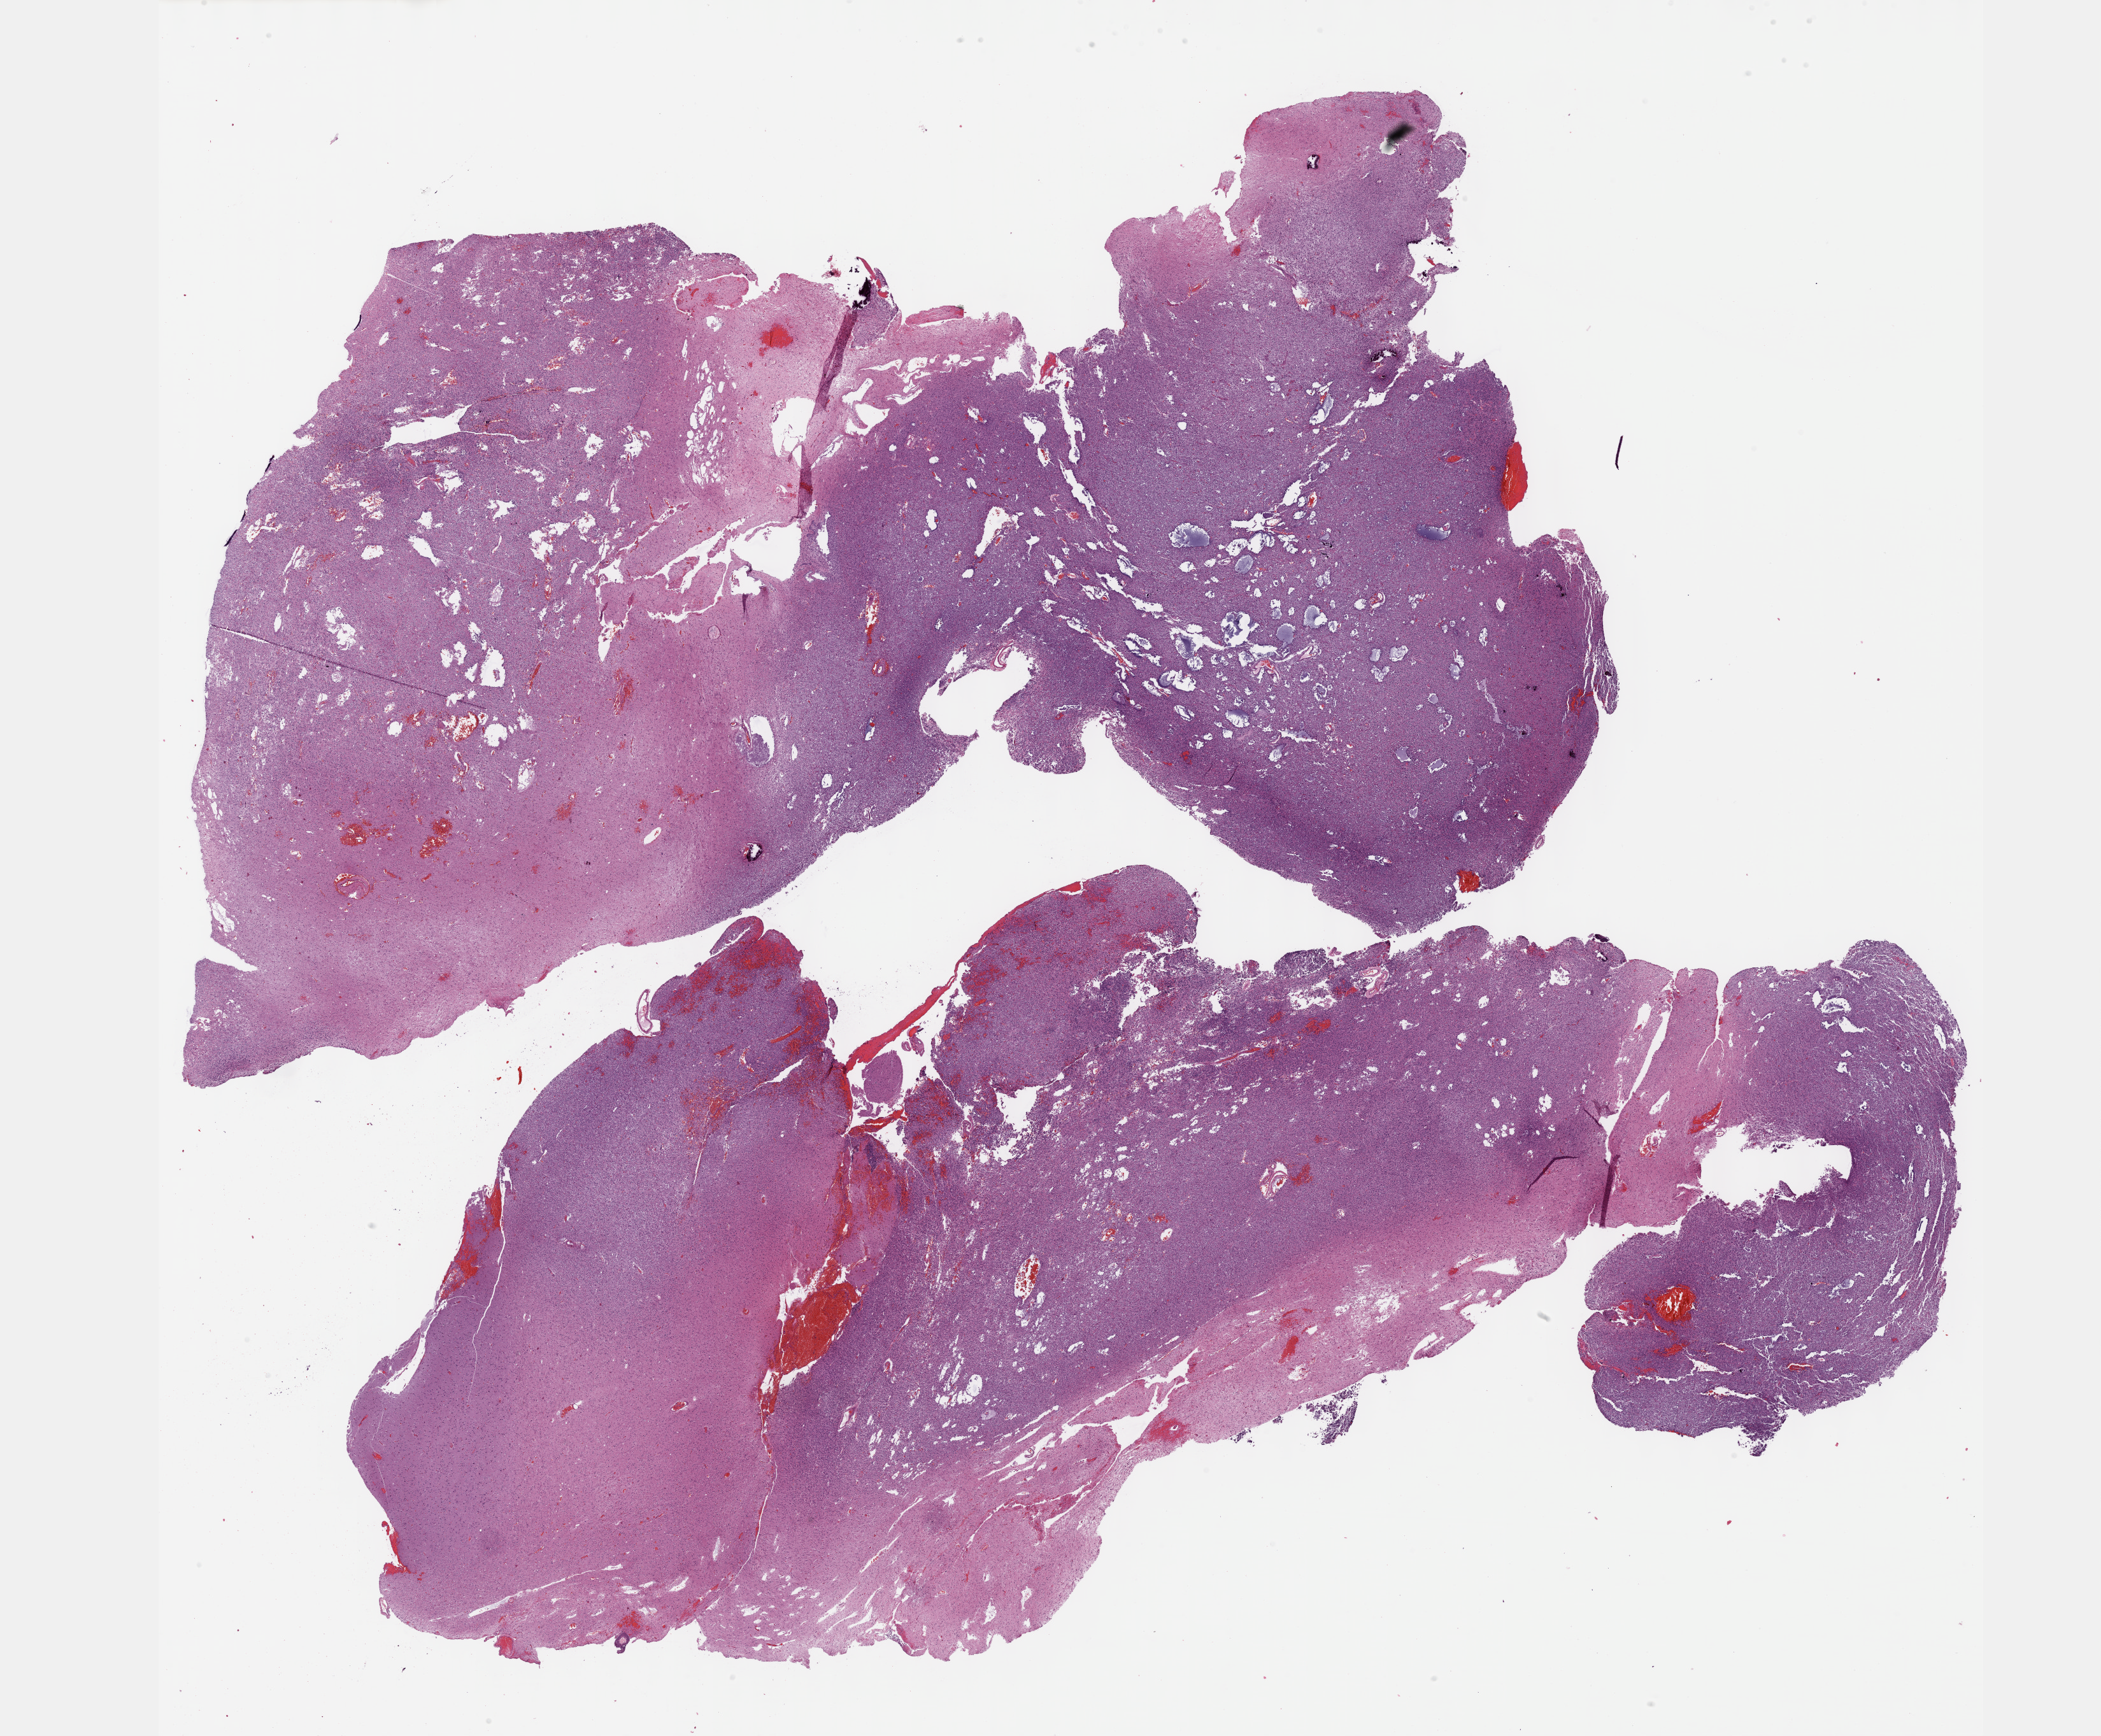
H&E-stained whole-slide image, low-resolution overview of the scanned area, about 26.7 x 22.0 mm (acquisition: 40x scan), FFPE section, brain, primary tumour sample. Male patient; age at initial diagnosis 60 years. Histologic grade: G3 (poorly differentiated).
- laterality: right
- histologic diagnosis: Oligodendroglioma, anaplastic (cerebrum)